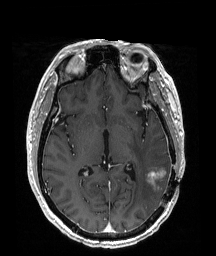
Brain MRI from a brain-tumour surgery series, one axial slice. Position 97 of 192 along the scan axis. T1-weighted post-contrast. 1 mm slice thickness. 216 × 256 image matrix, field of view 211 × 250 mm. Case-level facts recorded for this patient, not image findings: histopathology: Glioblastoma; WHO grade: 4; IDH mutation: no; tumour location: Left Temporoparietal.
Annotated regions visible in this slice (expert manual segmentation):
- tumour: bounding box <144,167,170,183> (left, top, right, bottom; pixels)